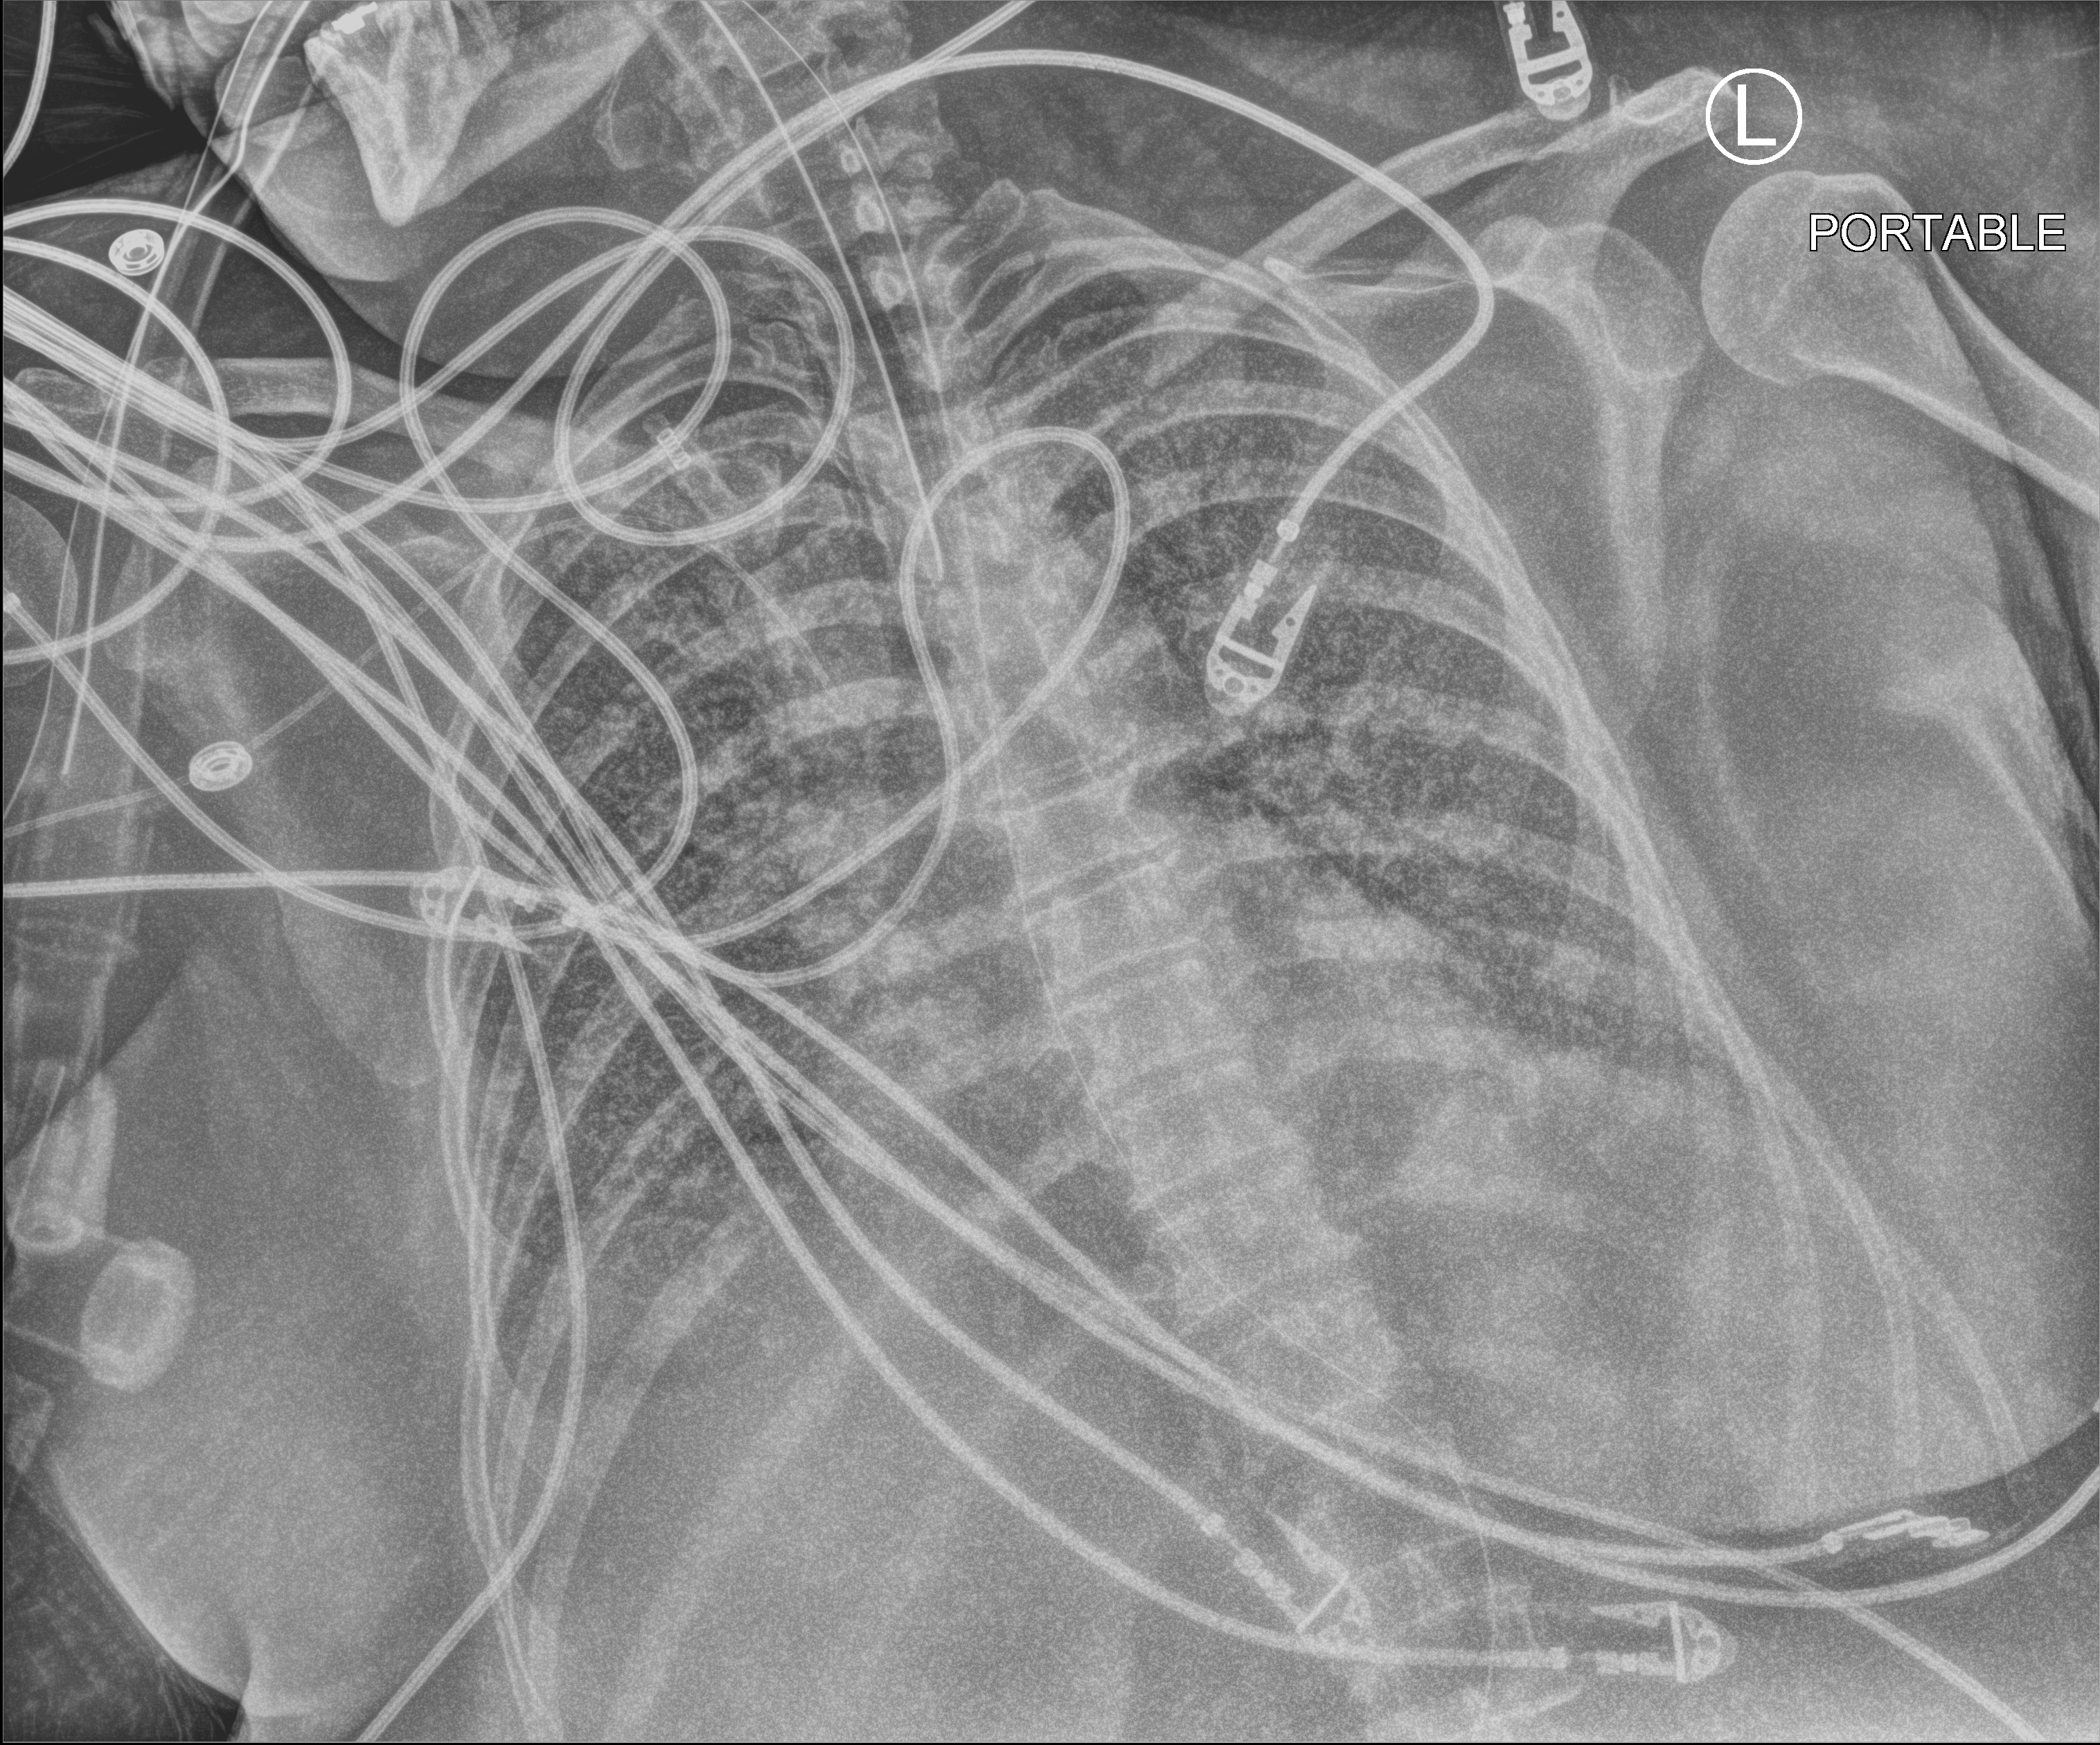
Bedside chest radiograph (computed radiography). Patient hospitalised with COVID-19; female, aged 18–59 years.
Admission-level facts for this patient (not findings on this image; timing relative to this image not recorded): chronic kidney disease (admission record): no; length of hospital stay: 95 days; smoking status (admission record): never.